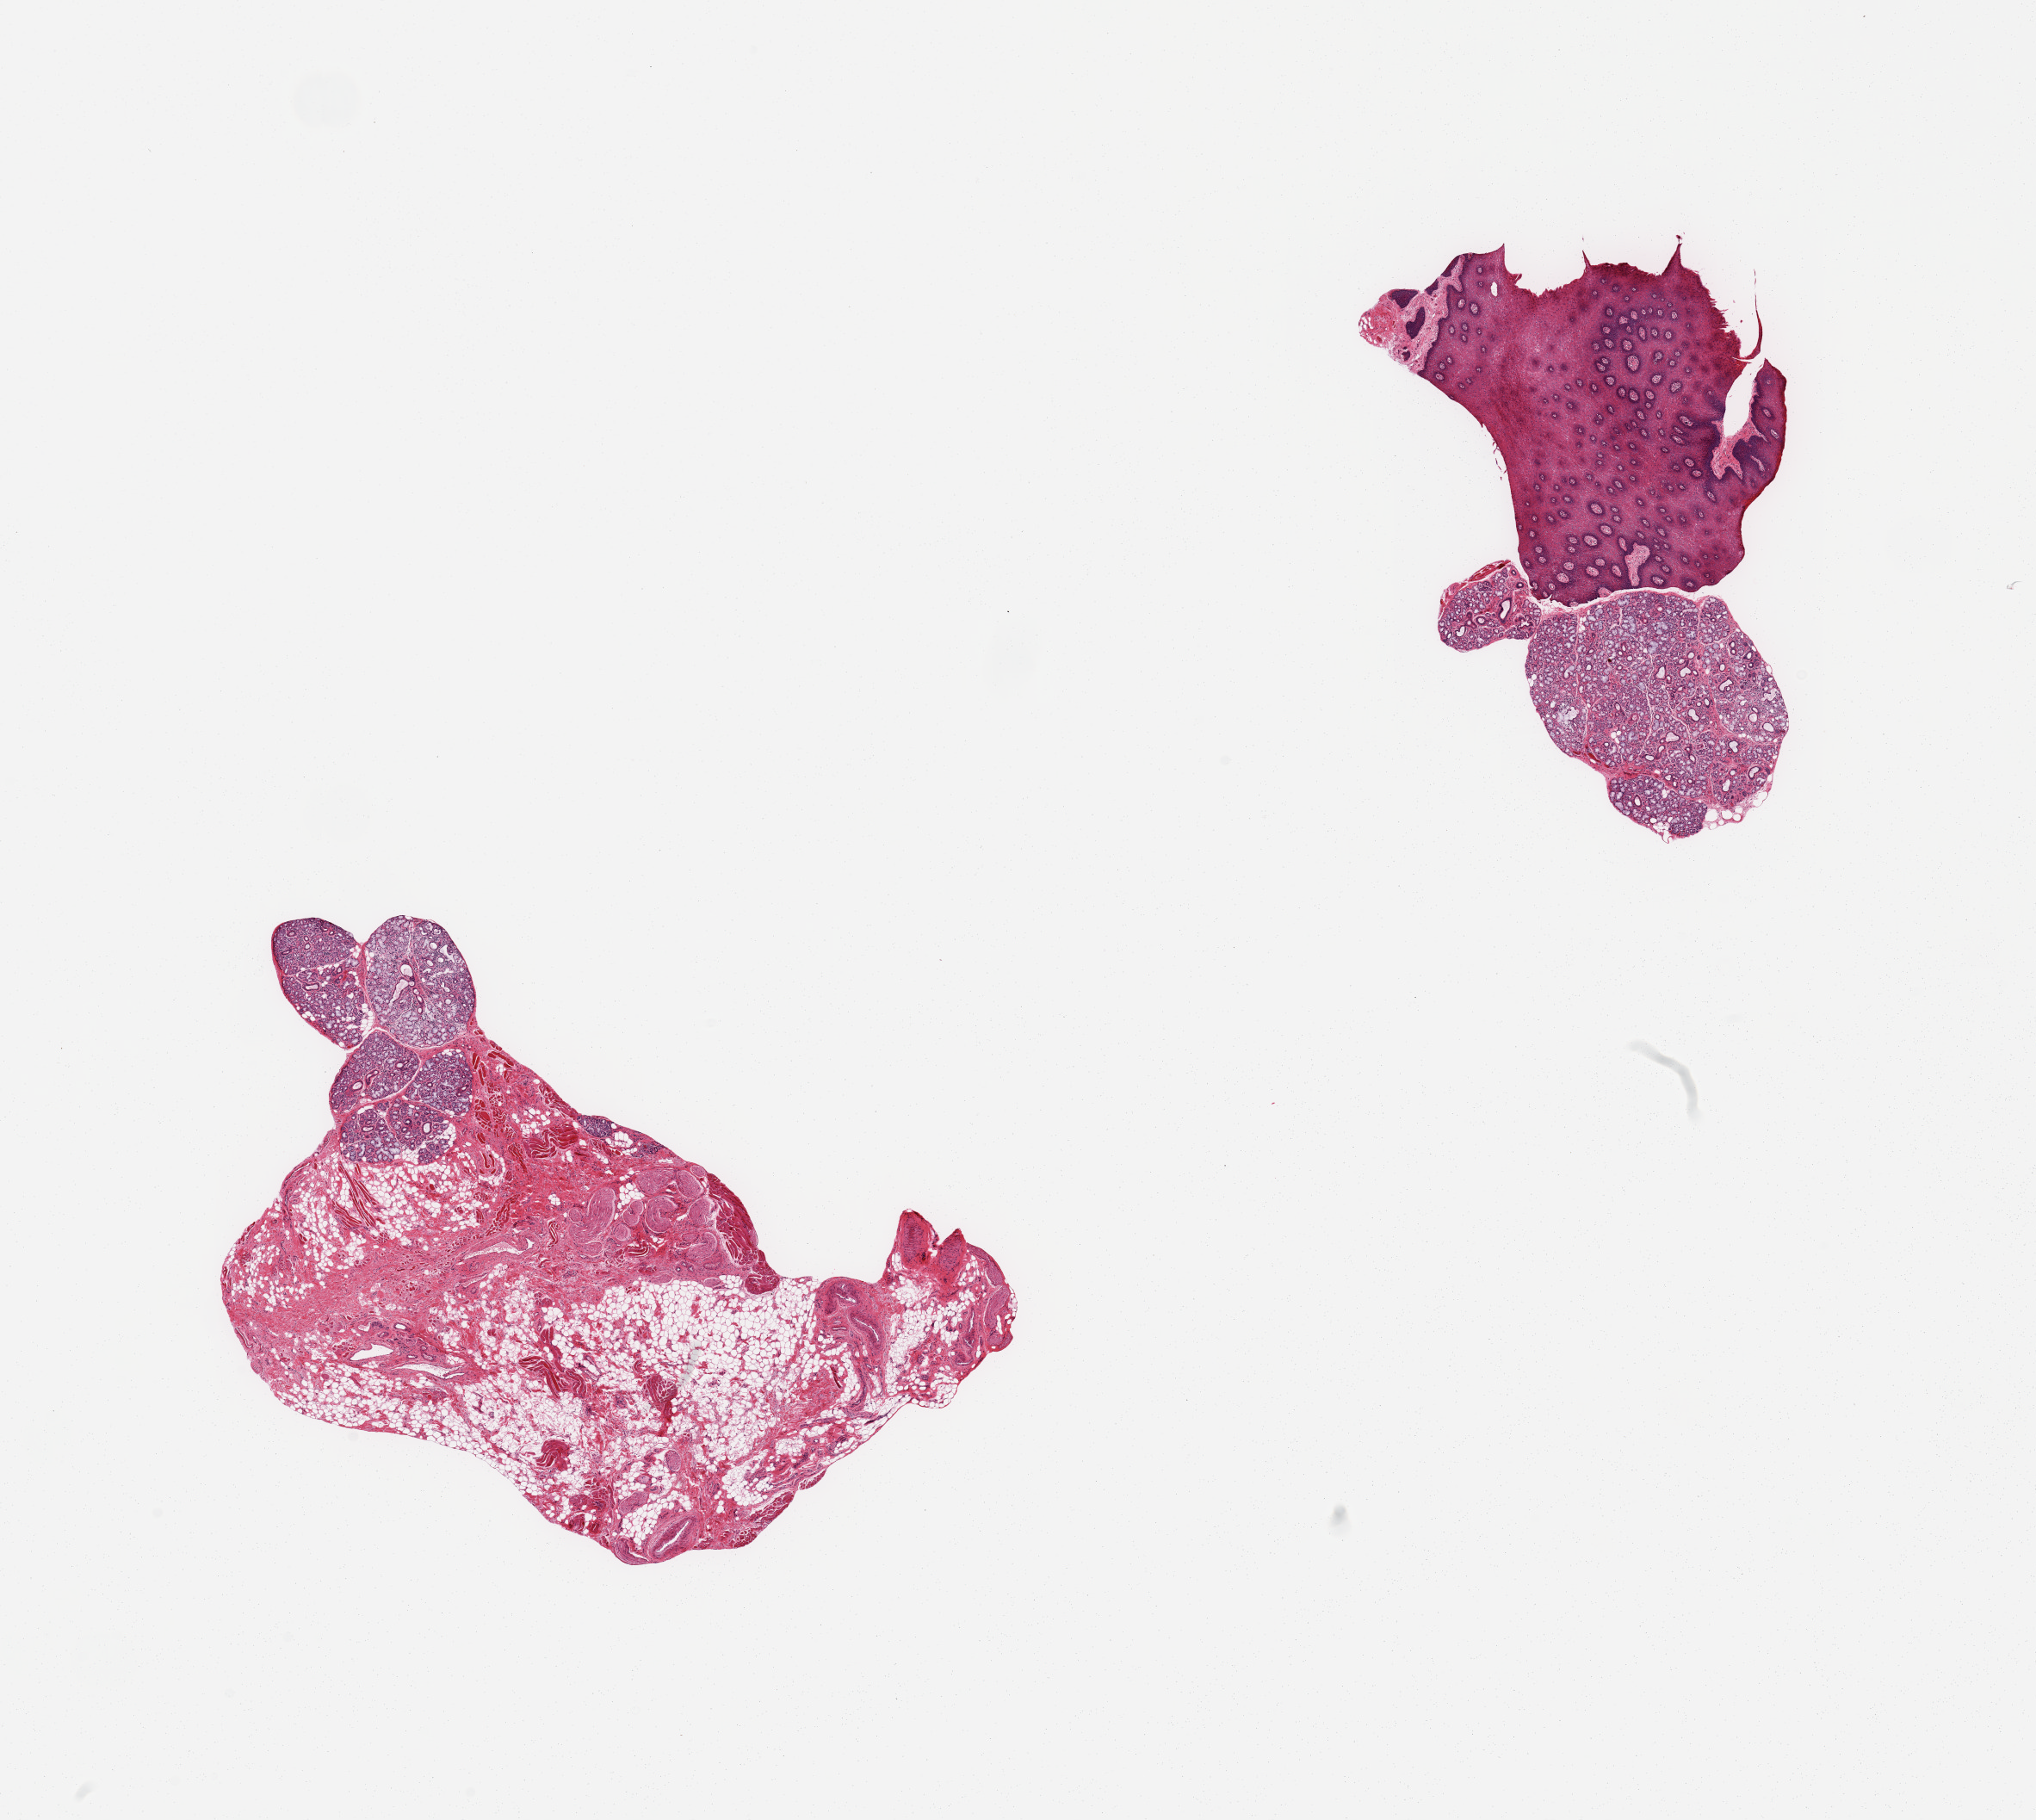
Digitized H&E-stained section — a low-resolution overview of the entire scanned area, about 18.7 x 16.7 mm; PAXgene-fixed paraffin-embedded (PFPE) section; sampled site (target tissue): minor salivary gland; tissue donor sample.
* pathologist's review note for this sample: 2 pieces; 1 with gland + 50% lip; other gland with 80% fibrofatty stroma; [glands]